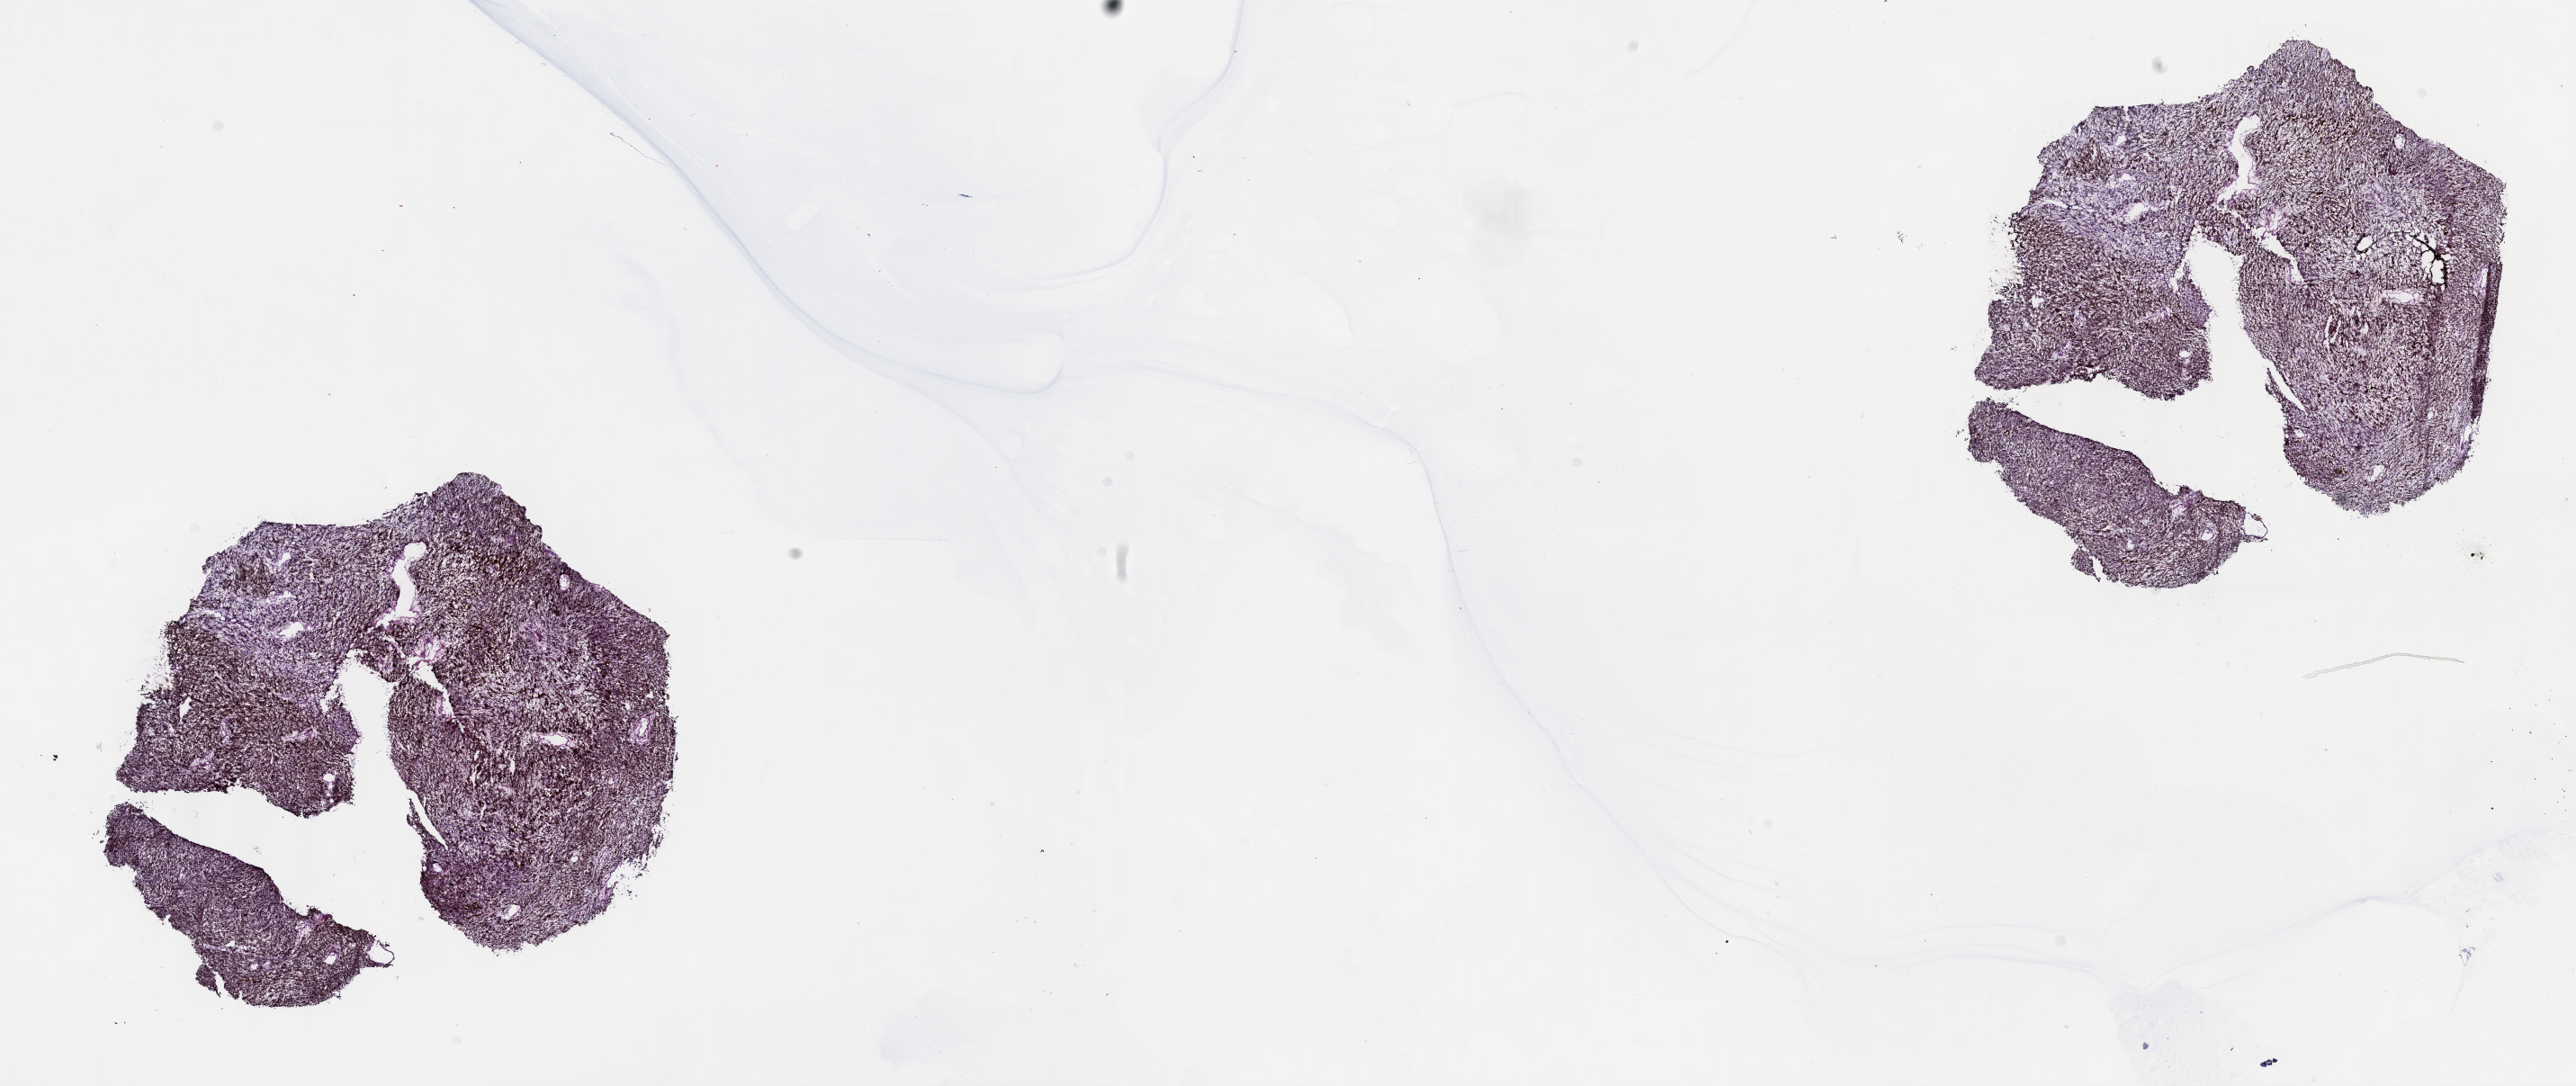
Digitized H&E tissue section (whole slide) — shown as a low-resolution overview of the whole scanned area (about 23.2 x 9.8 mm, acquisition: 40x scan); frozen section; primary tumour sample from the uvea. Female patient; age at initial diagnosis 78 years. Pathologist review of this section (percent, as recorded): tumour cells 100%, tumour nuclei 80%, normal cells 0%, stromal cells 0%, necrosis 0%. Inflammatory infiltration, as recorded: lymphocyte infiltration 1%, monocyte infiltration 0%, neutrophil infiltration 0%.
• diagnosis: Spindle cell melanoma, NOS (ciliary body)
• TNM: T3b N0 M0
• laterality: right
• AJCC pathologic stage: IIIA (7th edition)